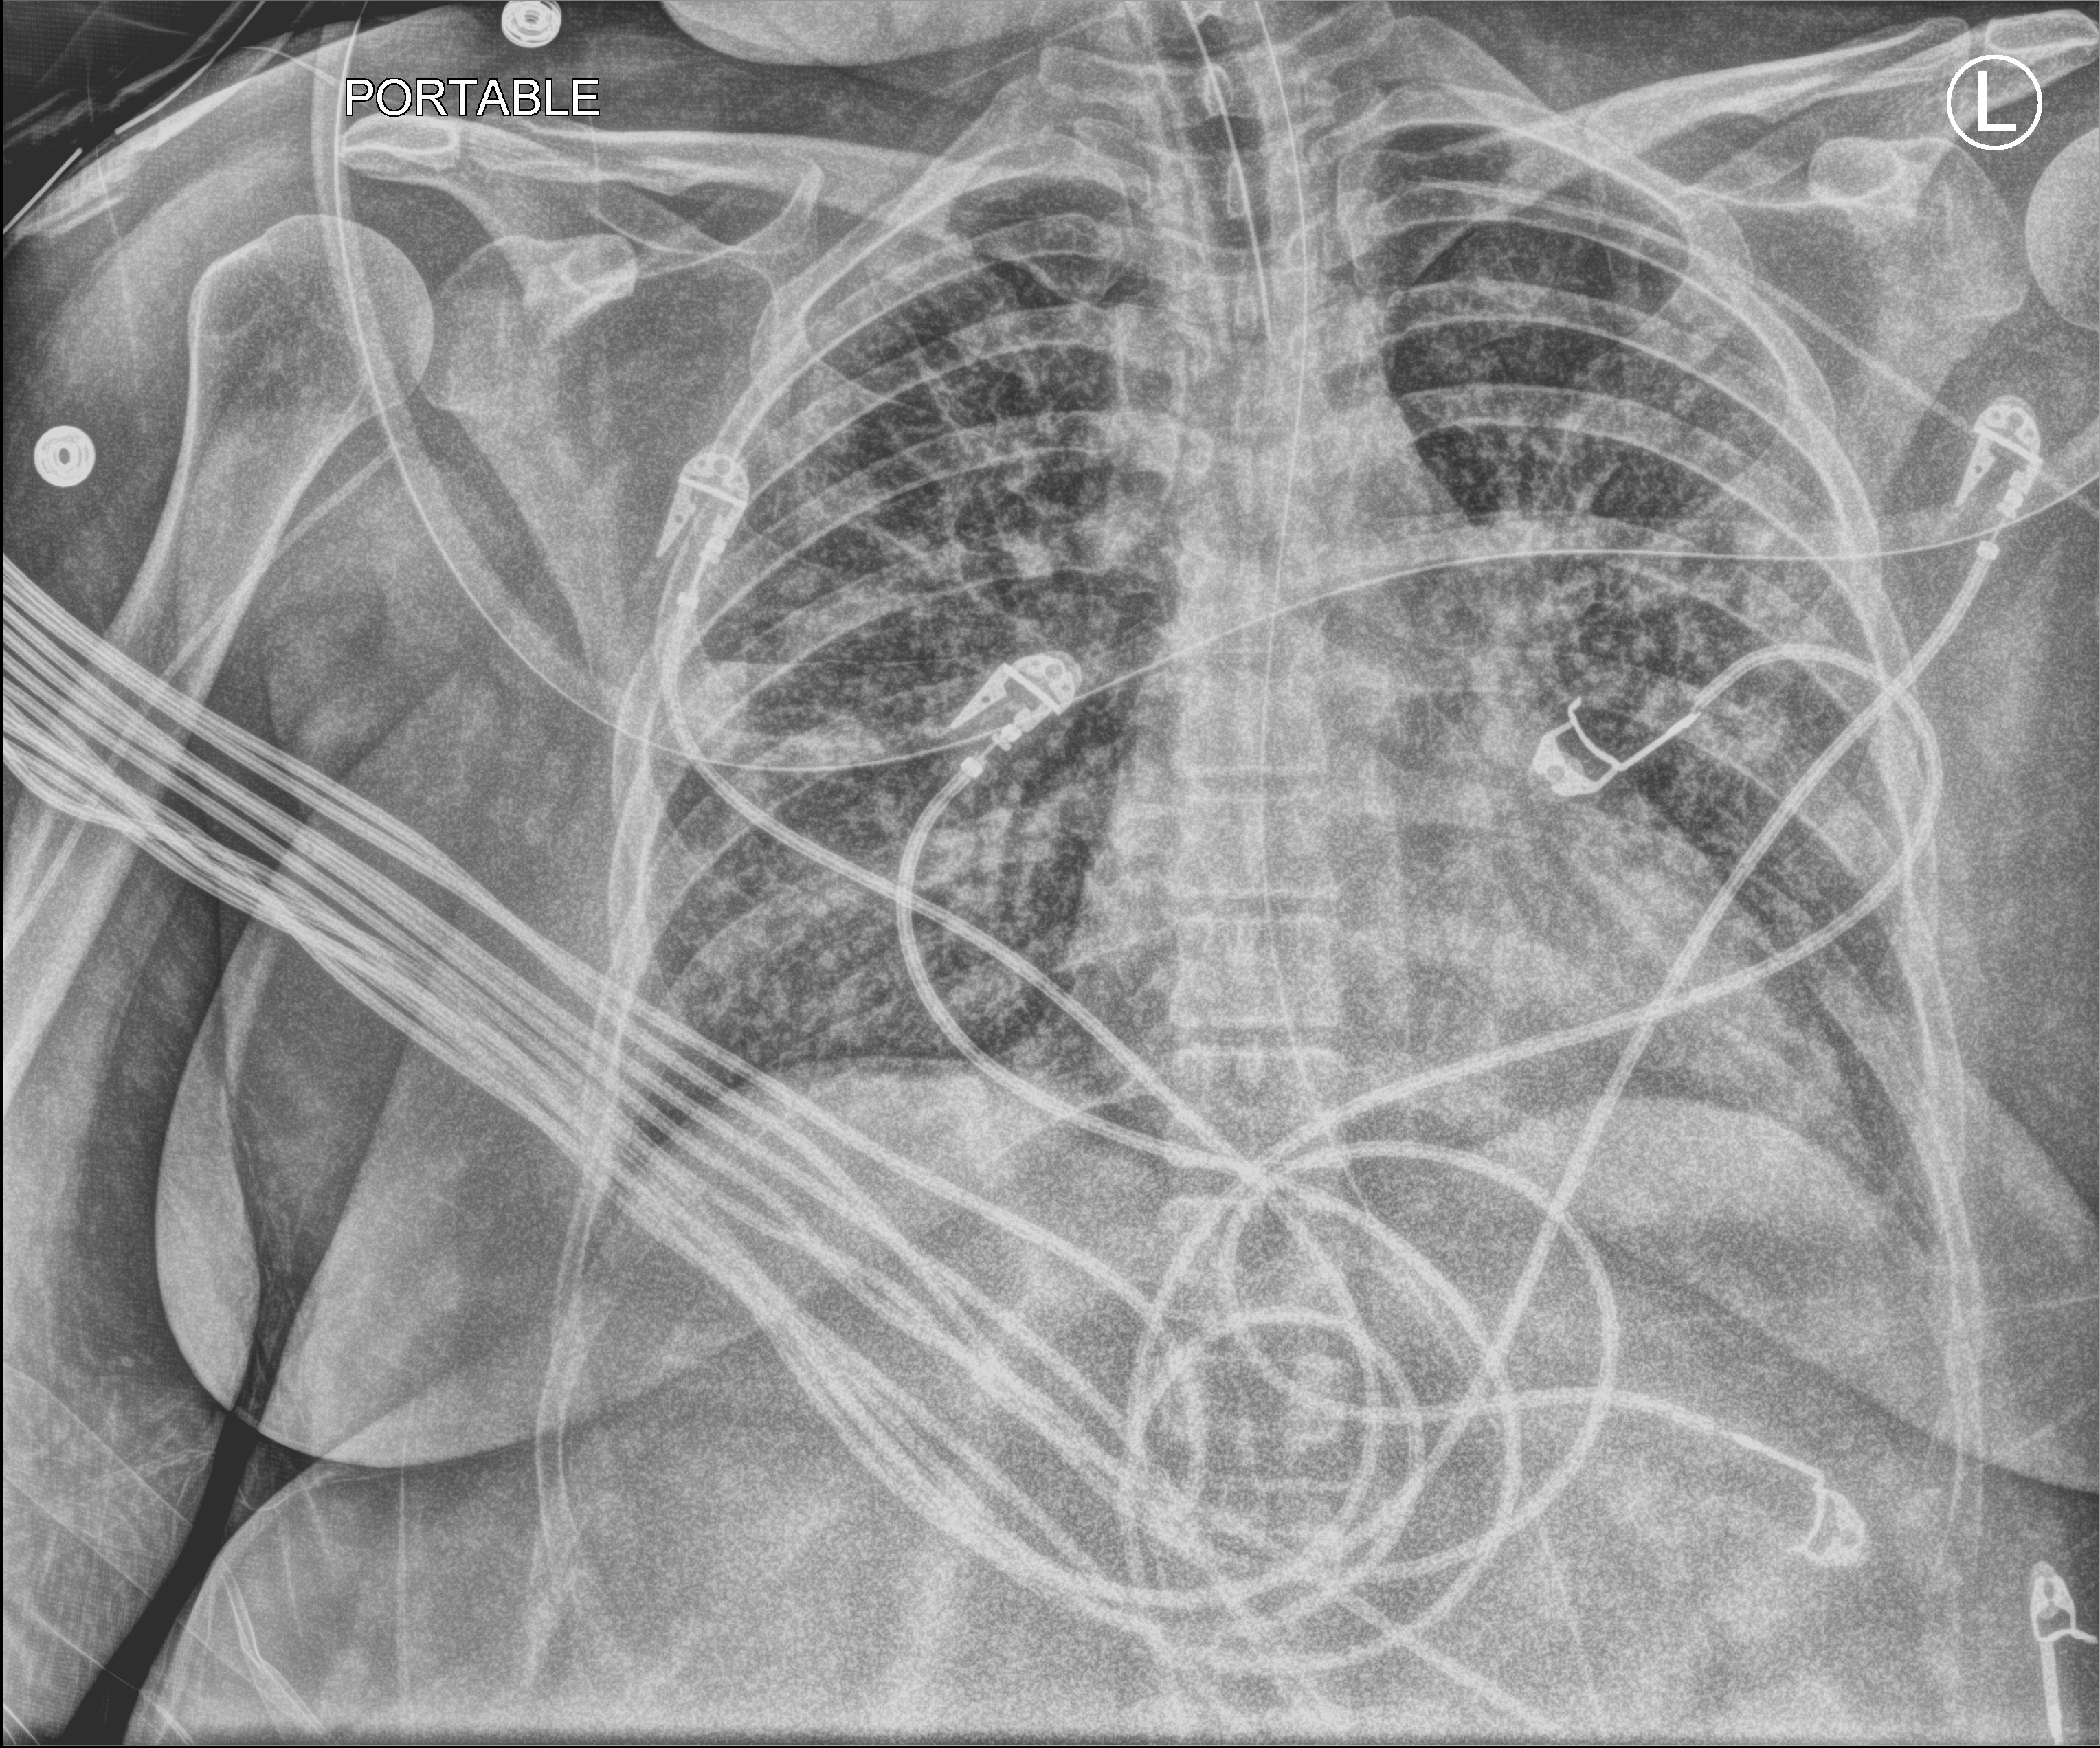
Portable chest radiograph, anteroposterior (AP) projection. Female patient hospitalised with COVID-19, age 18–59 years.
Admission-level facts for this patient (not findings on this image; timing relative to this image not recorded):
- admitted to intensive care during this hospital stay: yes